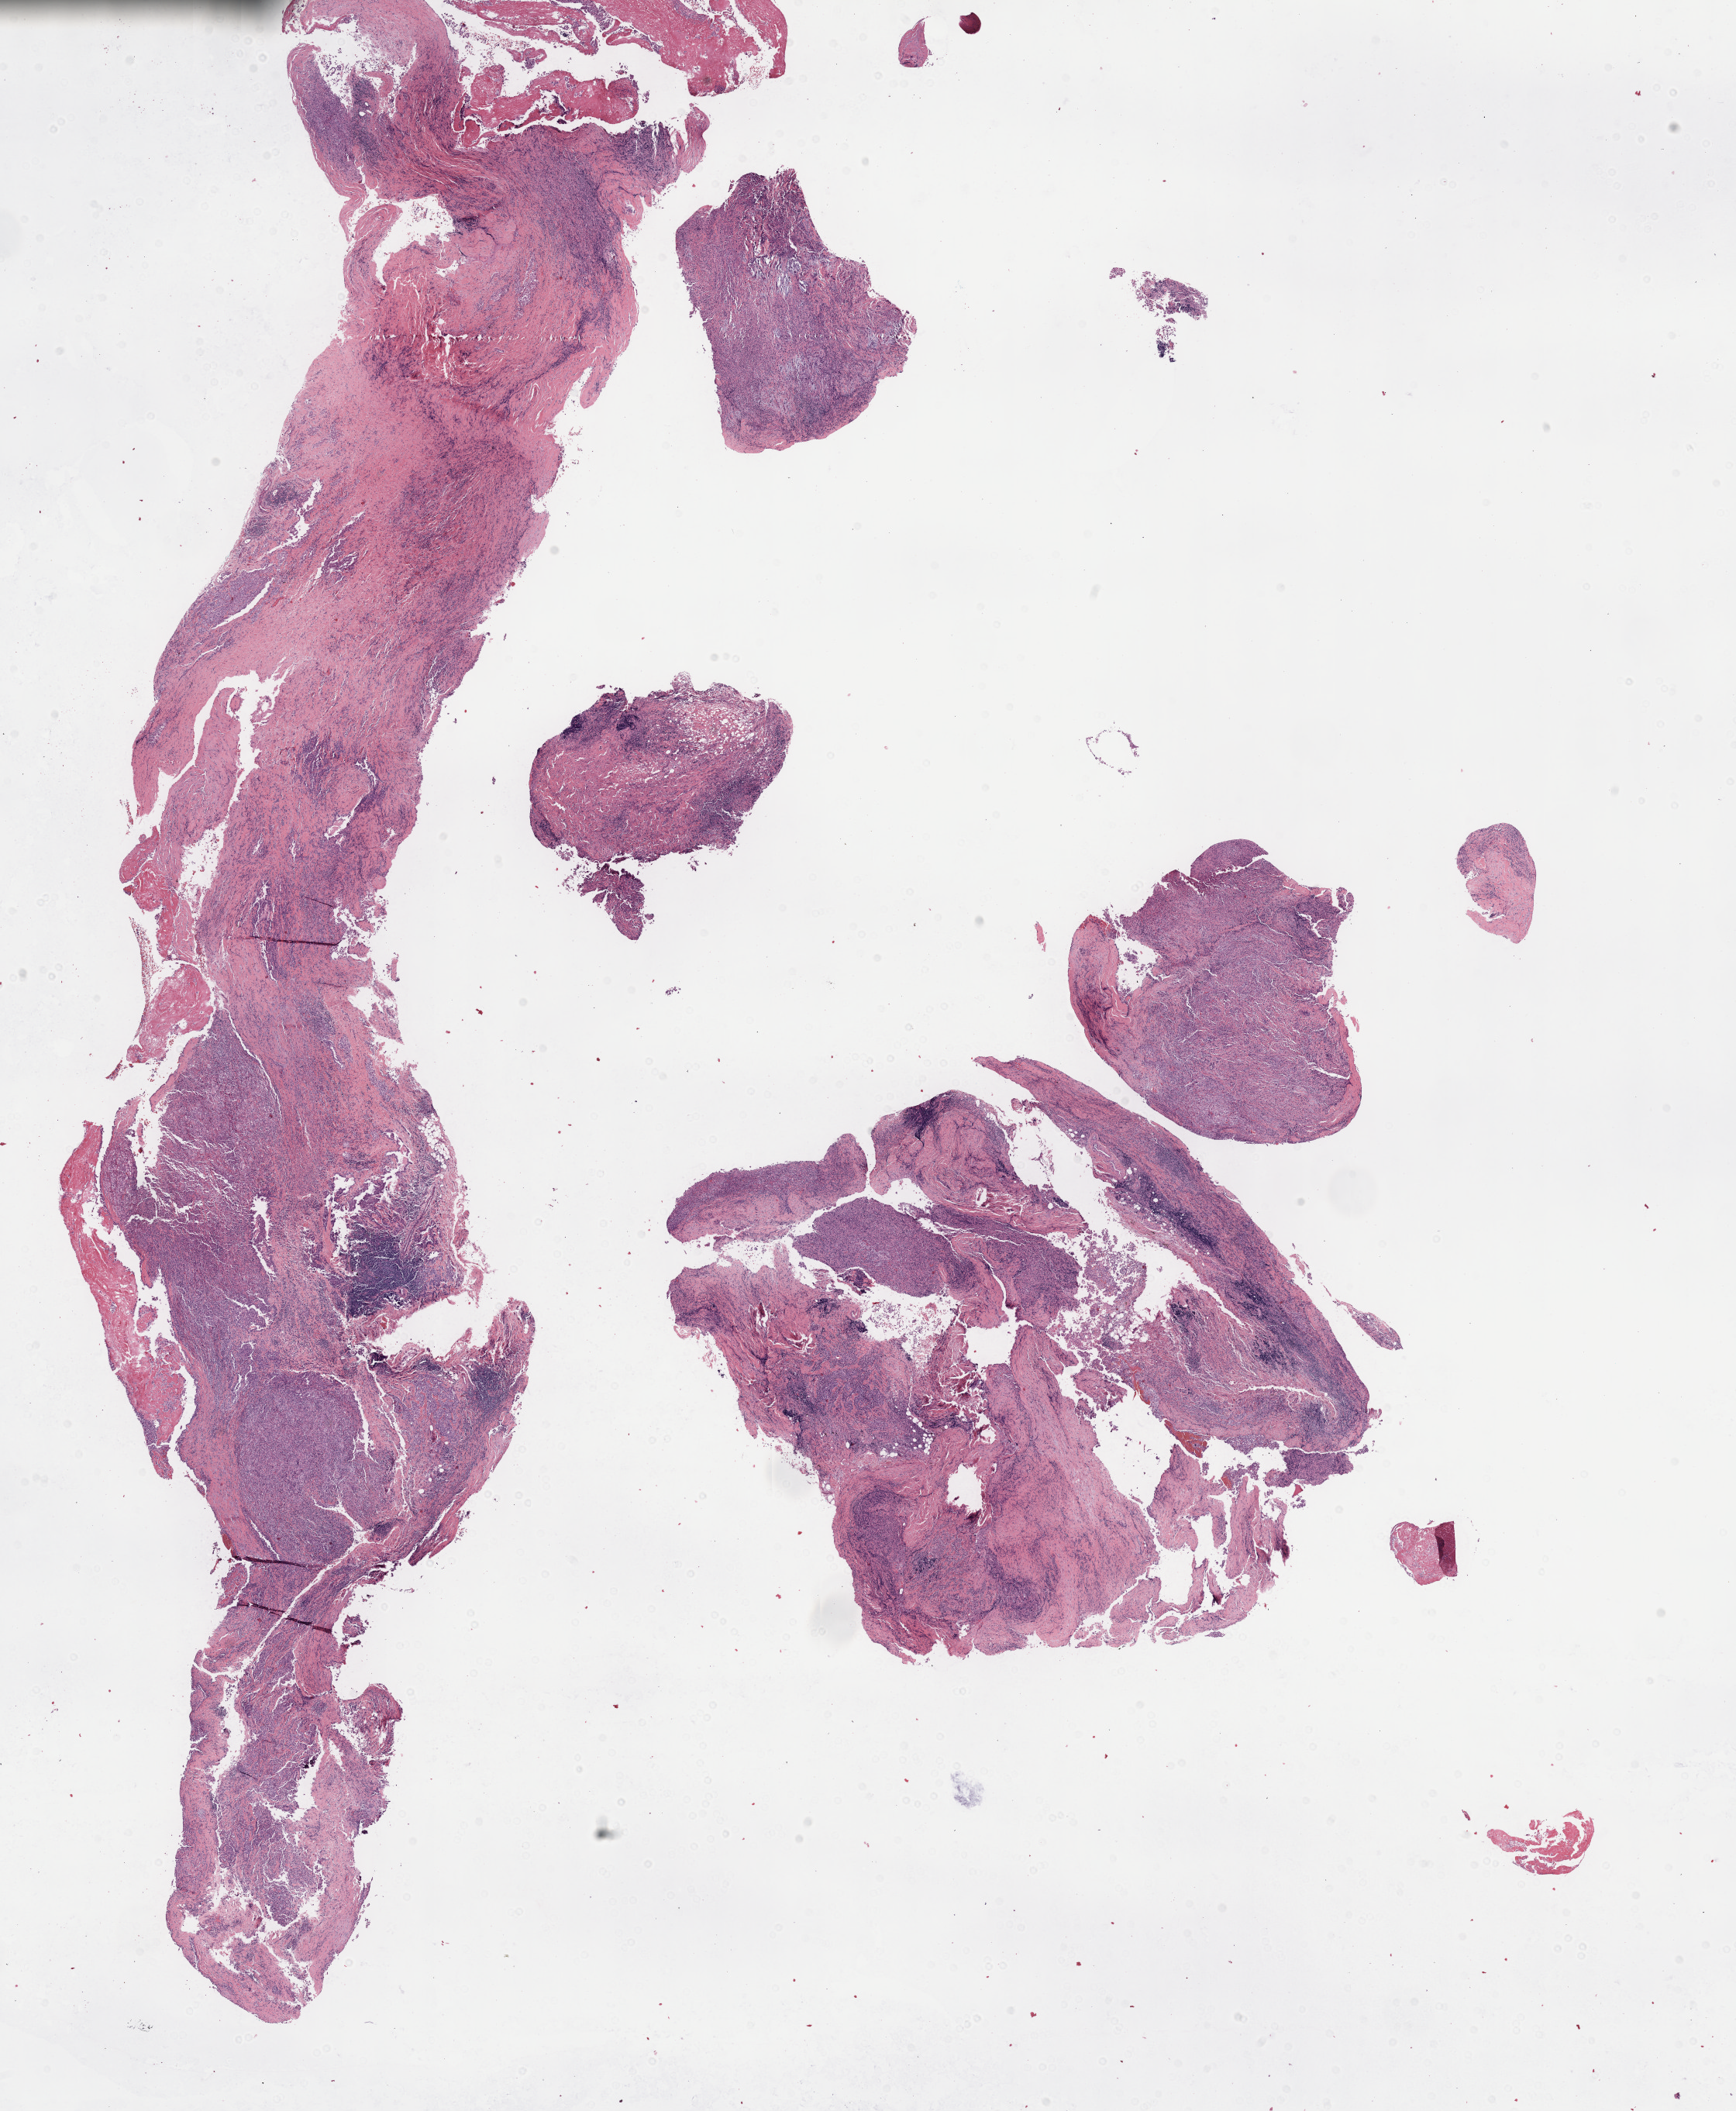
Digitized Hematoxylin and eosin (H&E) stained tissue section (whole slide) — low-resolution overview of the scanned area, about 18.1 x 22.0 mm (slide scanned at 40x); formalin-fixed paraffin-embedded (FFPE) diagnostic section; mesothelium, primary tumour sample. Male patient; age at initial diagnosis 66 years.
Laterality: right. AJCC pathologic stage: IV (7th edition). TNM: T1b N0 M1. Diagnosis: Mesothelioma, malignant (pleura, NOS).